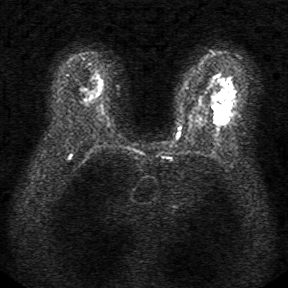
Breast MRI, one axial slice. Slice 22 of 34 in the series (ordered by position). Diffusion-weighted series; image 2 of 4 stored at this slice position (different b-values; order by instance number). 1.5 T. 5 mm slice thickness. 288 × 288 image matrix. Female patient.
Annotated regions visible in this slice (outlined manually by an expert reader):
- tumour on diffusion-weighted imaging: bounding box [x1, y1, x2, y2] px = [213, 107, 229, 123]